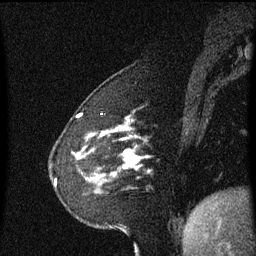
Breast MRI (dynamic contrast-enhanced), one sagittal slice. Position 14 of 60 along the scan axis. Dynamic contrast-enhanced series, image 2 of 3 at this slice position (ordered by acquisition). 1.5 T. TE 4.2 ms, TR 8.4 ms. 2.2 mm slice thickness. 256 × 256 image matrix. Patient: female, 60 years. From the clinical record (not read from this slice): setting: breast cancer imaged before/during neoadjuvant chemotherapy; receptor status: triple-negative.
Annotated regions visible in this slice (semi-automatically segmented with operator editing):
- analysis volume of interest (the breast-tissue region the enhancement analysis was run in; not a lesion): bounding box [x1, y1, x2, y2] px = [72, 148, 138, 193]
- tumour enhancement mask (voxels above the 70 % enhancement threshold inside the analysis volume of interest): [124, 150, 138, 165]